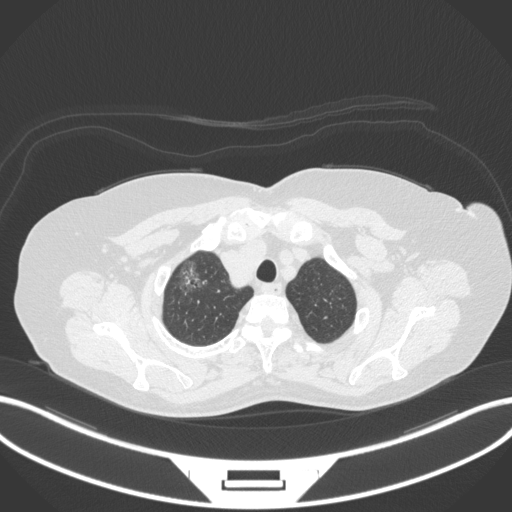
Chest CT, one axial slice; slice 308 of 365 in the series (ordered by position); reconstruction kernel B31f; lung window (W 1500 / L -600 HU); 1 mm slice thickness; 512 × 512 image matrix, field of view 400 × 400 mm. Female patient, age 62 years. From the clinical record (not read from this slice): clinical TNM (as recorded): T1c N0 M0.
Structures marked on this image (bounding box drawn by a radiologist):
- lung tumour (recorded histology: adenocarcinoma): bounding box (x1, y1, x2, y2) in pixels: (172, 254, 212, 300)